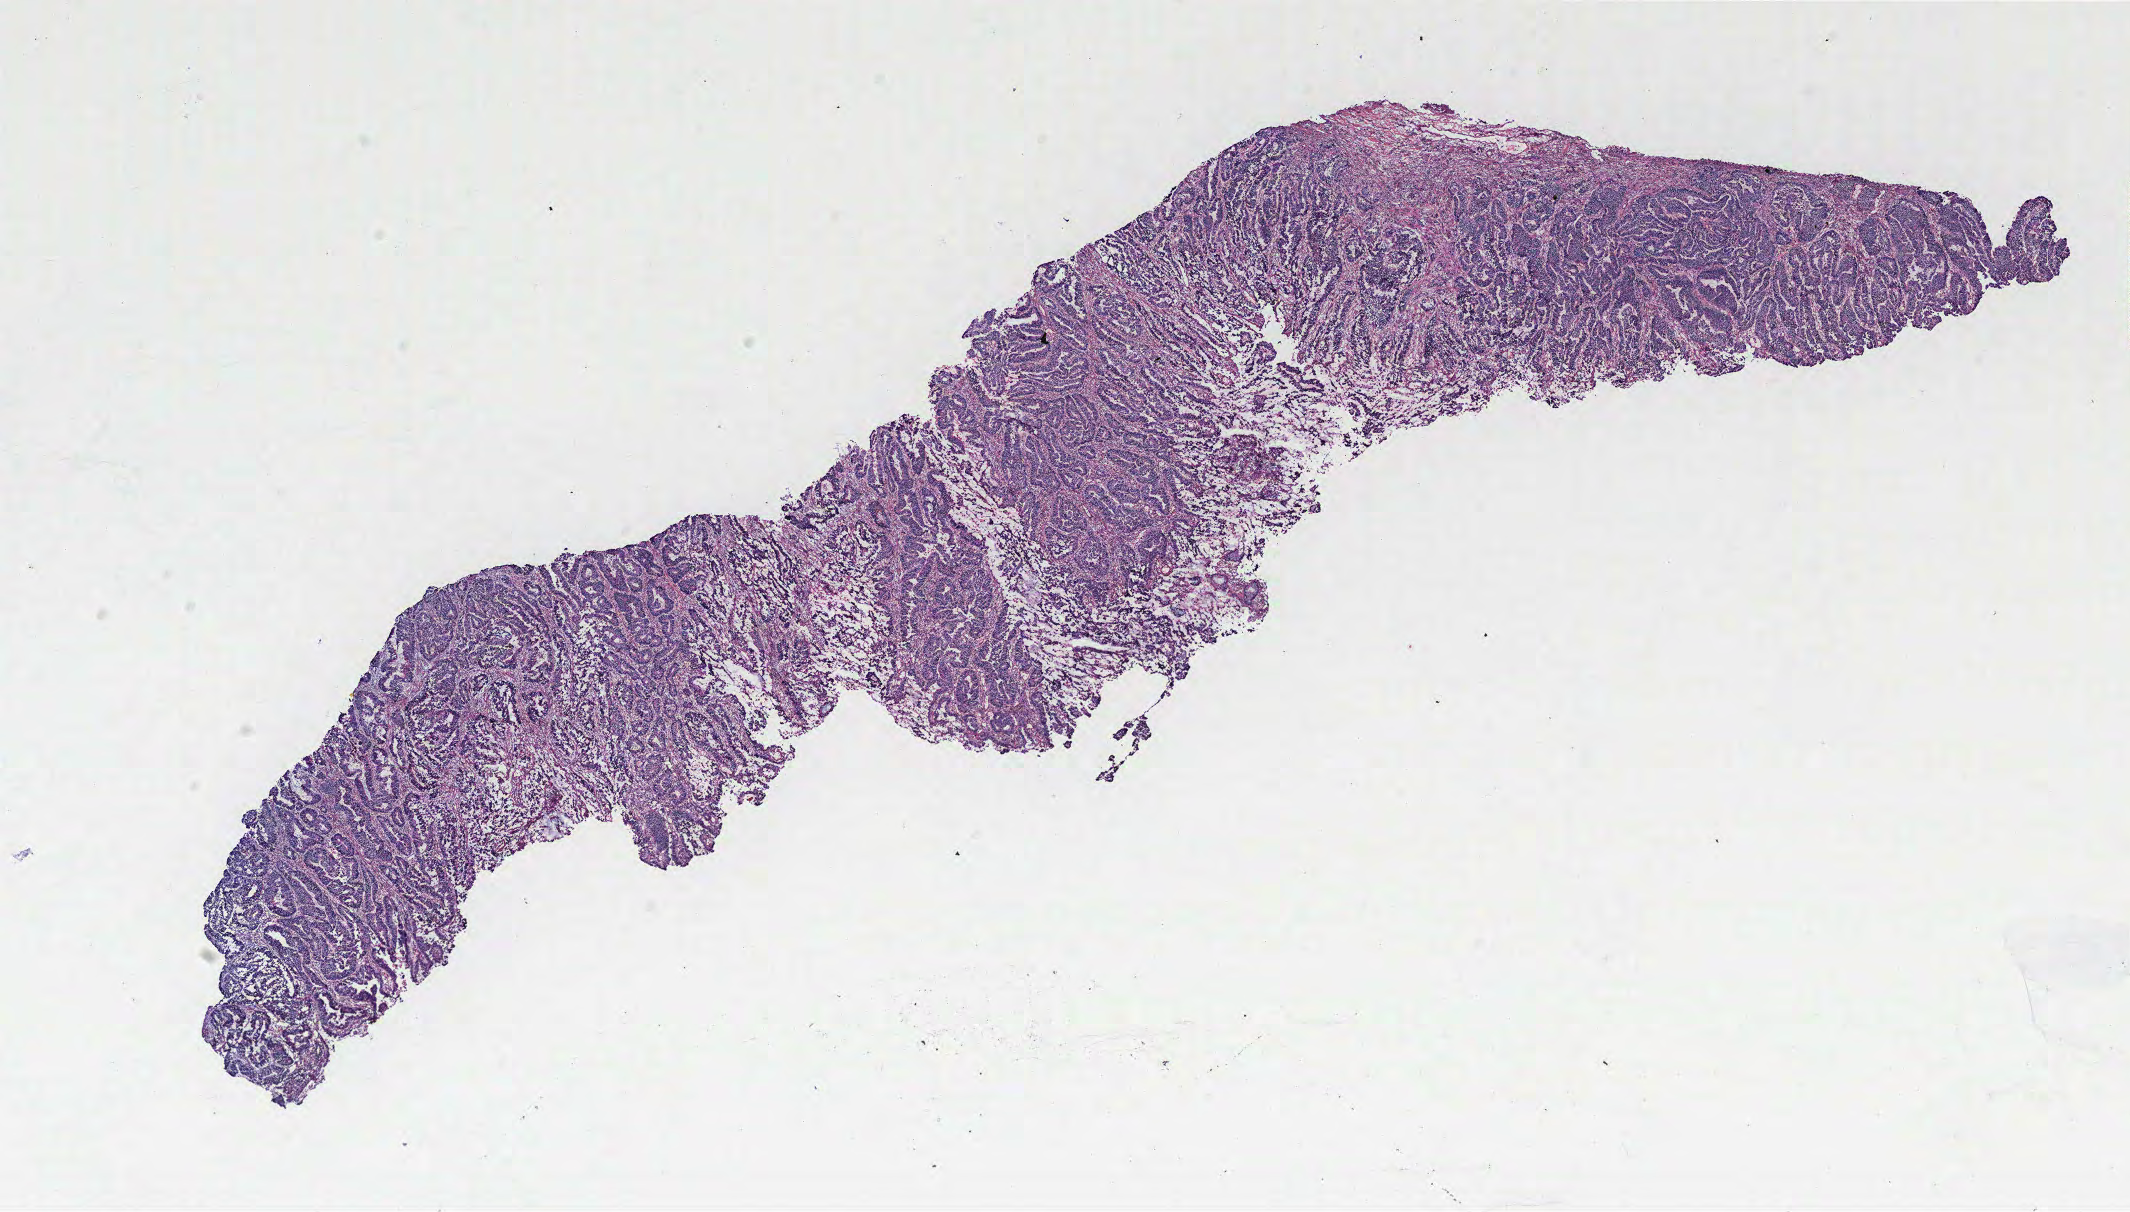
Whole-slide histology image, H&E — shown as a low-resolution overview of the whole scanned area (about 17.0 x 9.7 mm), colon, tissue type not recorded.
Patient diagnosis (cohort enrolment): colon cancer (colon).